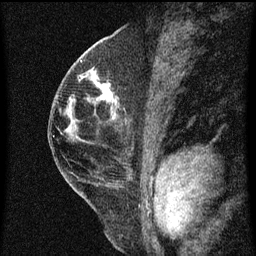
Breast MRI (dynamic contrast-enhanced), one sagittal slice. Slice 31 of 60 in the series (ordered by position). Dynamic contrast-enhanced series, image 2 of 3 at this slice position (ordered by acquisition). 1.5 T. TE 4.2 ms, TR 8 ms. 256 × 256 image matrix. Patient: female, 48 years.
Structures marked on this image (semi-automatically segmented with operator editing):
- analysis volume of interest (the breast-tissue region the enhancement analysis was run in; not a lesion): box from (x=89, y=72) to (x=120, y=113) px
- tumour enhancement mask (voxels above the 70 % enhancement threshold inside the analysis volume of interest): (x=95, y=76)–(x=118, y=105)